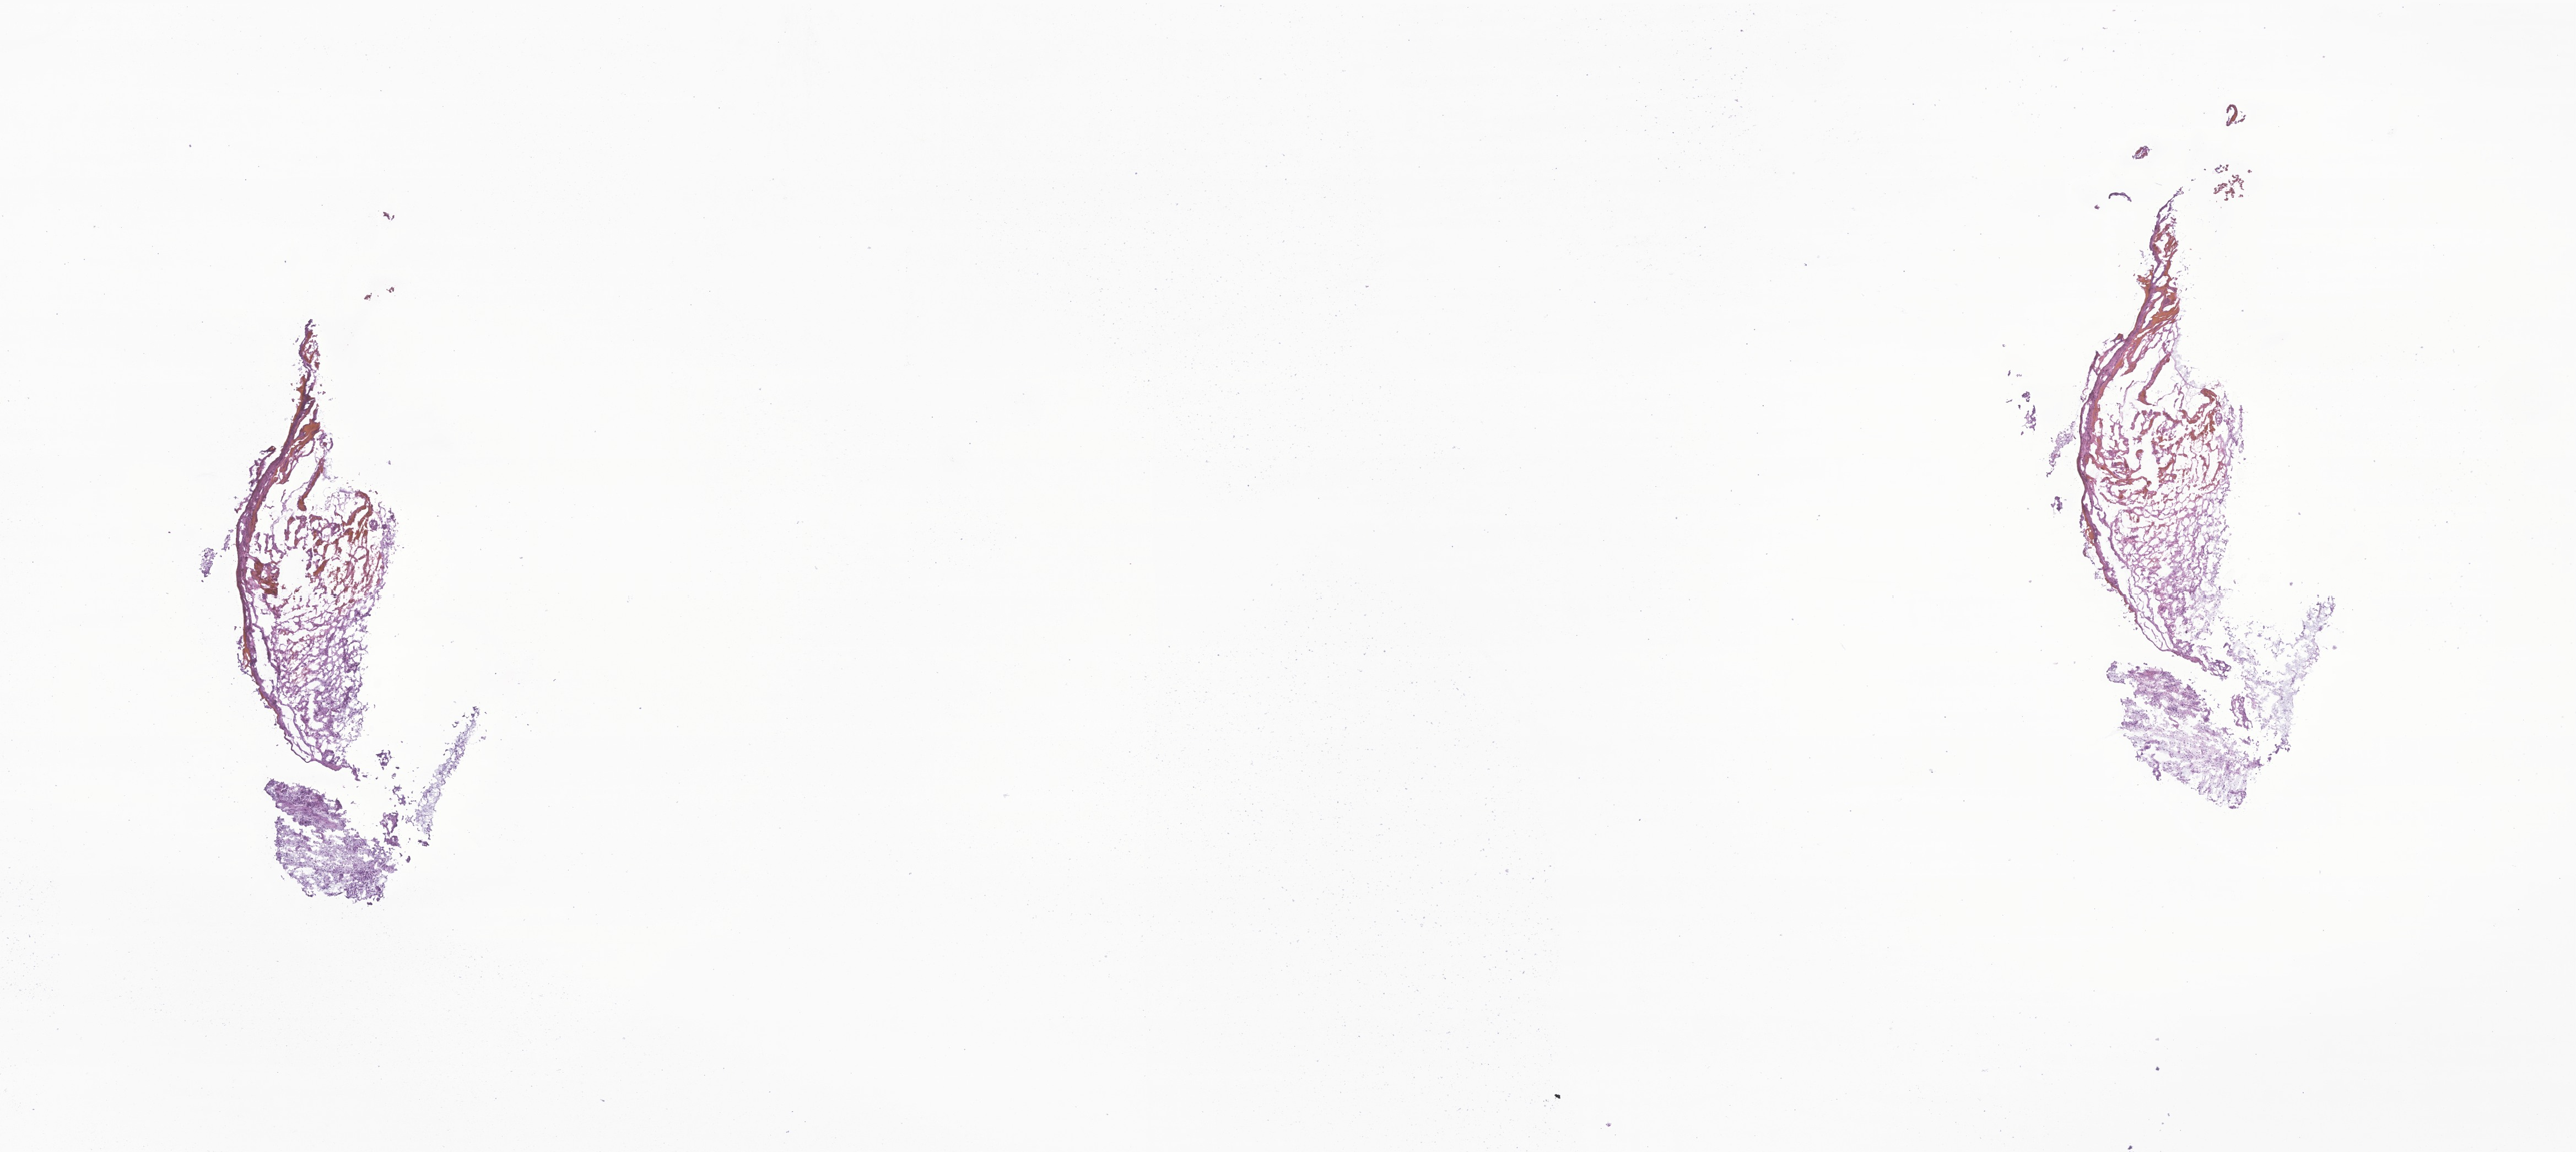
Digitized H&E-stained section of tumor tissue from the brain, low-resolution overview of the scanned area, about 19.7 x 8.8 mm, frozen section (OCT-embedded). Patient female; age 88 months (7 years 4 months).
Diagnosis (ICD-O-3 morphology term): Oligoastrocytoma, NOS.